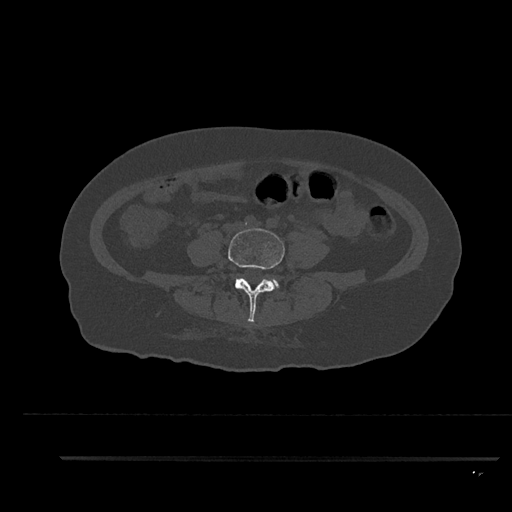
CT including the spine, one axial slice; position 8 of 797 along the scan axis; bone window (W 1800 / L 400 HU); 0.5 mm slice thickness; 512 × 512 image matrix, field of view 408 × 408 mm. Patient: female, 44 years. Case-level facts recorded for this patient, not image findings: primary cancer: renal.
Structures marked on this image (semi-automatically segmented with operator editing):
- L4 vertebra: bounding box <228,228,285,322> (left, top, right, bottom; pixels)